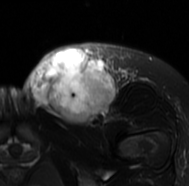
MRI of an extremity soft-tissue mass, one axial slice. Position 40 of 77 along the scan axis. T2-weighted fat-saturated. MR volume resampled by the dataset authors to the PET/CT grid (not the native acquisition matrix). 3.27 mm slice thickness. 189 × 186 image matrix, field of view 185 × 182 mm. Female patient. Case-level facts recorded for this patient, not image findings: histological type: leiomyosarcoma; grade: high; site of the primary tumour: groin.
Outlined on this slice (expert contour drawn on MRI and transferred to this co-registered scan by the dataset authors):
- gross tumour volume including surrounding oedema: box from (x=24, y=41) to (x=135, y=128) px
- gross tumour volume (mass): (x=29, y=47)–(x=116, y=124)